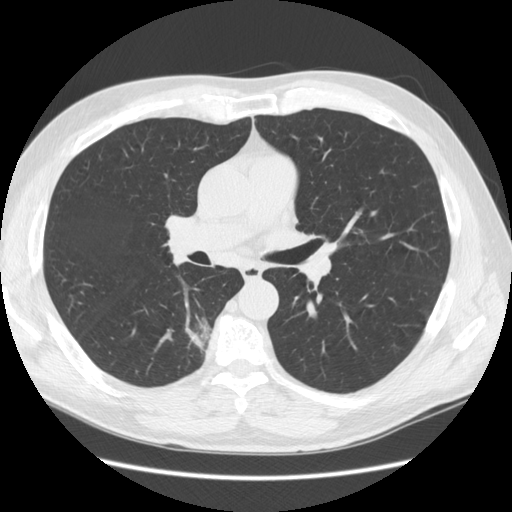
Low-dose screening chest CT, one axial slice; 120 kVp; lung window (W 1500 / L -600 HU); 512 × 512 image matrix, field of view 370 × 370 mm.
Outlined on this slice (outlined manually by an expert reader):
- lesion 1 (tumor, lower lobe of right lung): bounding box <192,314,213,343> (left, top, right, bottom; pixels)